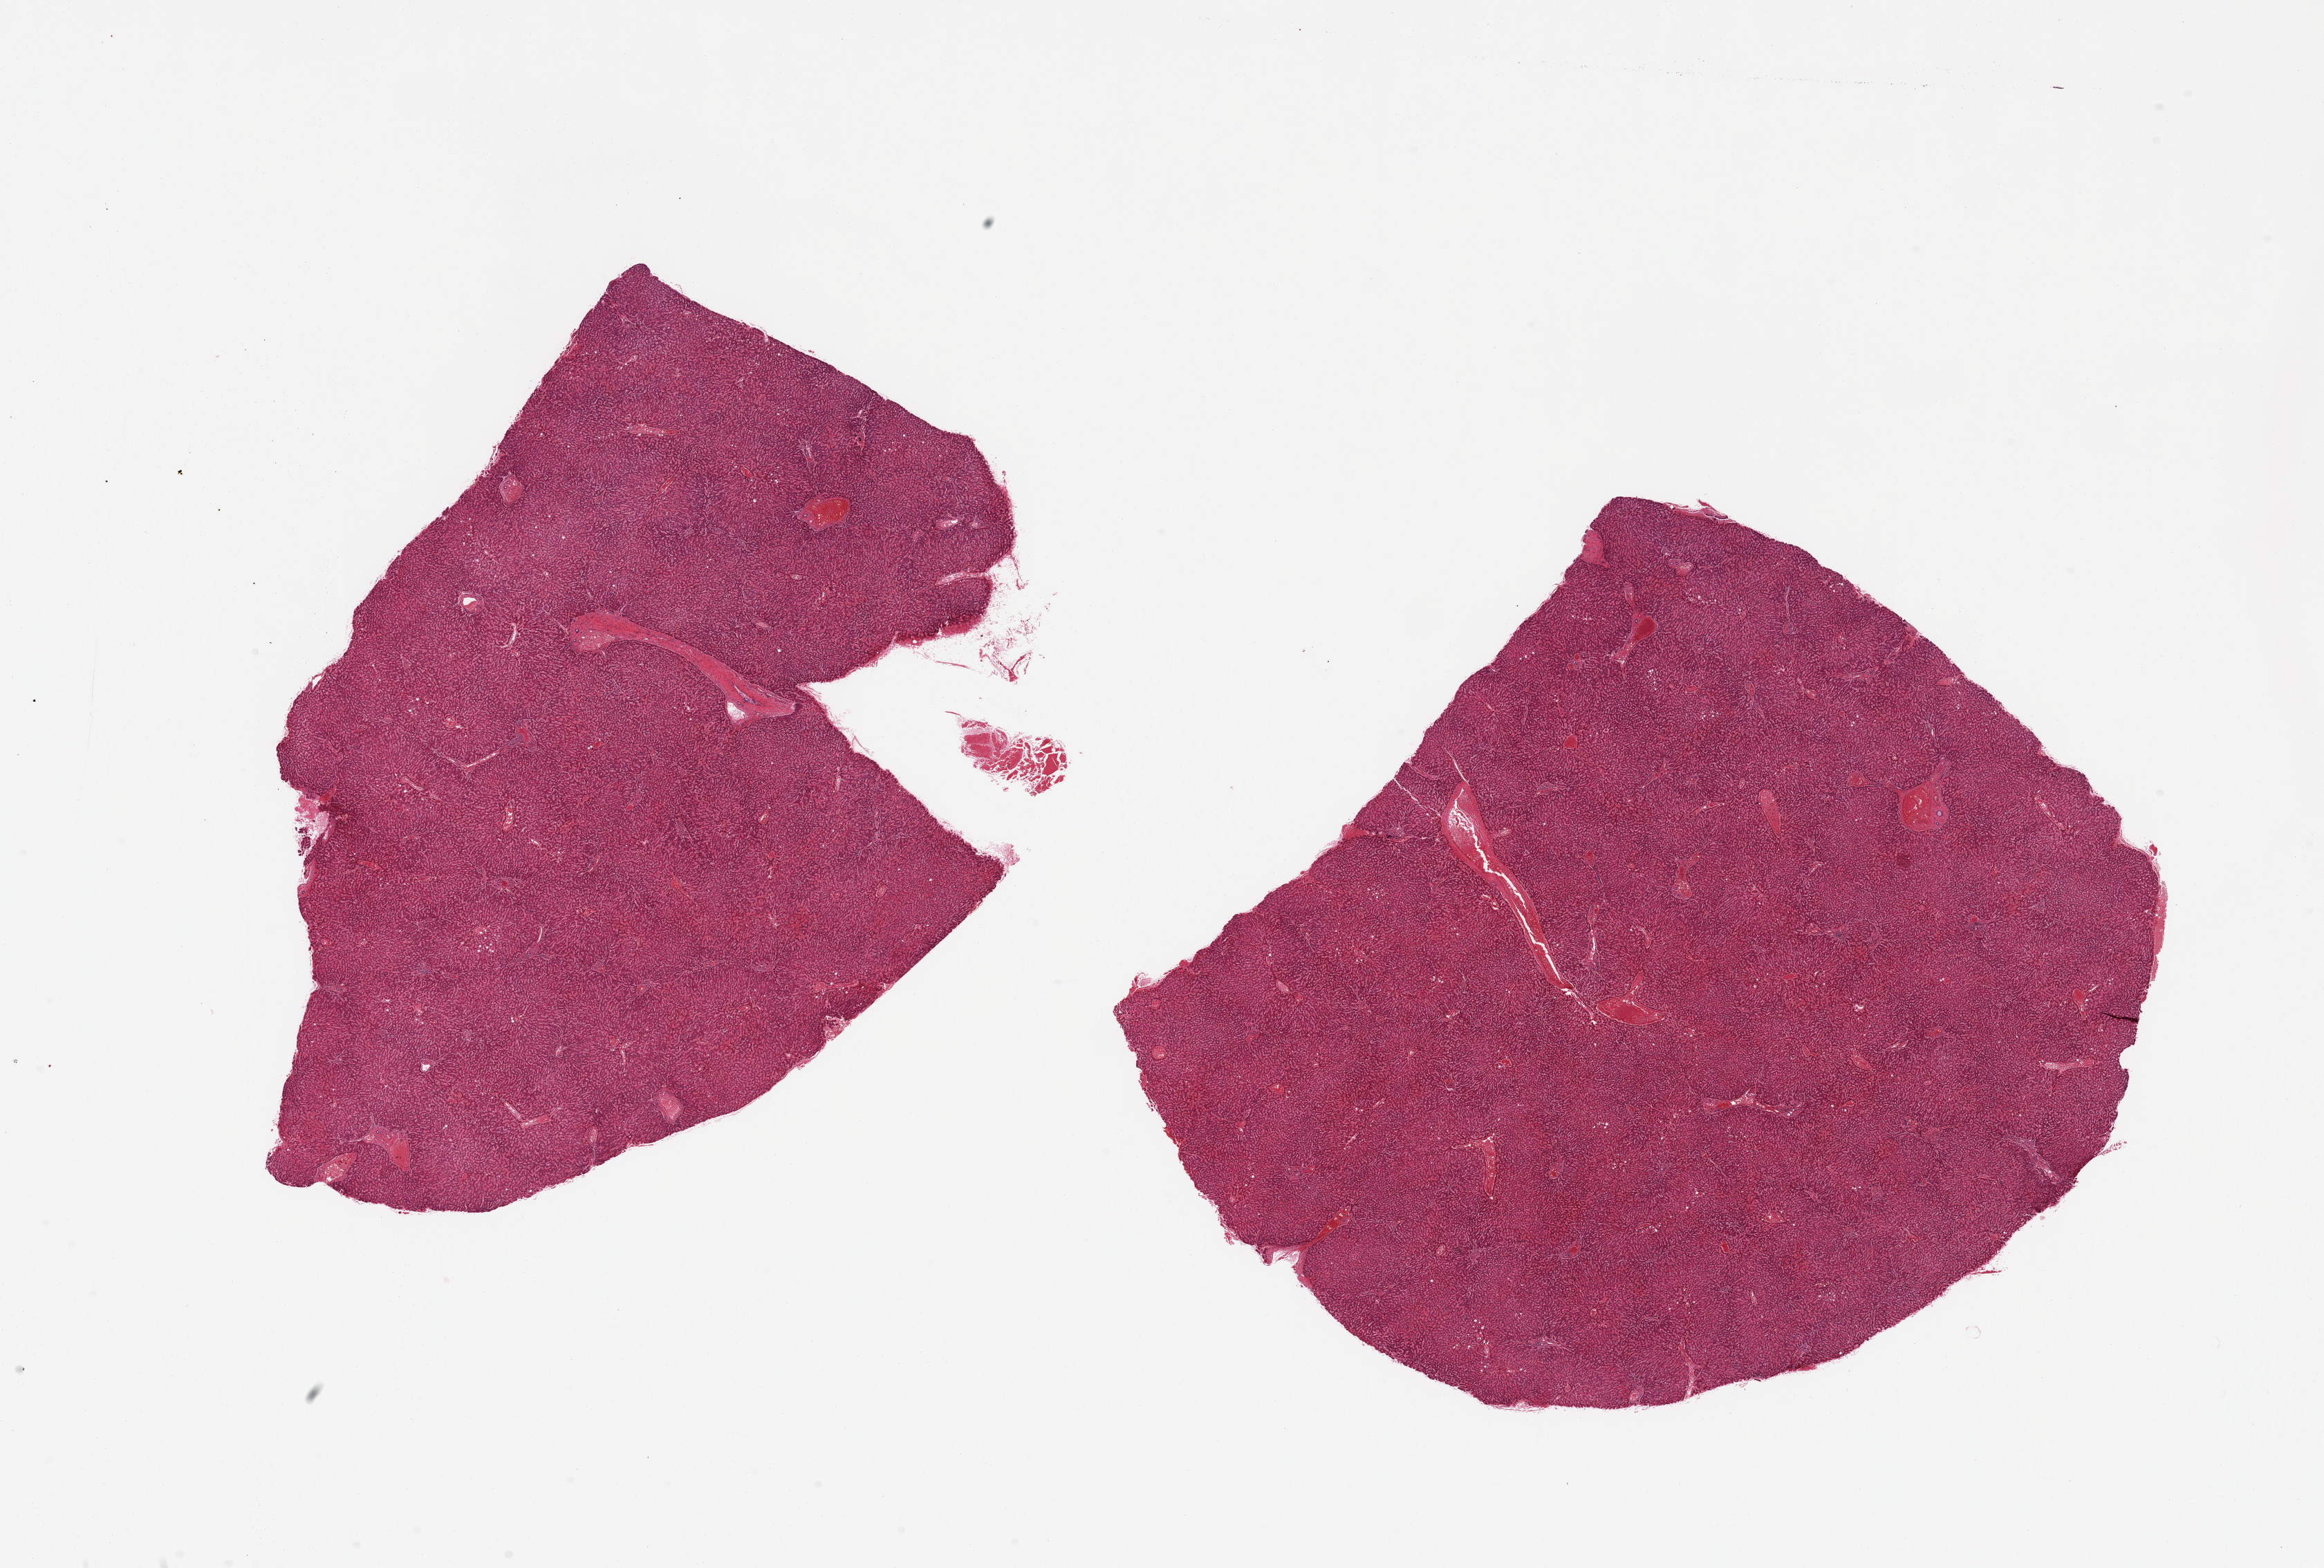
Haematoxylin and eosin whole-slide image, shown as a low-resolution overview of the whole scanned area (about 26.6 x 17.9 mm); PAXgene-fixed paraffin-embedded (PFPE) section; sampled site (target tissue): liver; donor tissue sample. Donor: male.
Reviewer comment on this tissue sample: 2 pieces; marked congestion.